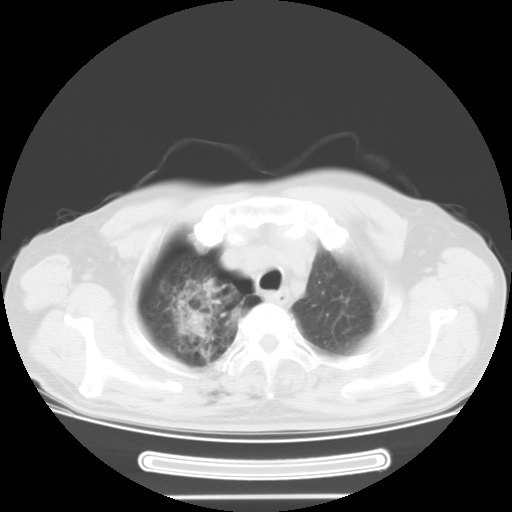
Chest CT, one axial slice. Position 25 of 29 along the scan axis. Lung window (W 1500 / L -600 HU). 10 mm slice thickness. 512 × 512 image matrix. Patient: male, 61 years. Case-level facts recorded for this patient, not image findings: clinical TNM (as recorded): T1c N3 M1b.
Annotated regions visible in this slice (rectangle marked by the reading radiologist):
- lung tumour (recorded histology: adenocarcinoma): bounding box <166,274,245,355> (left, top, right, bottom; pixels)